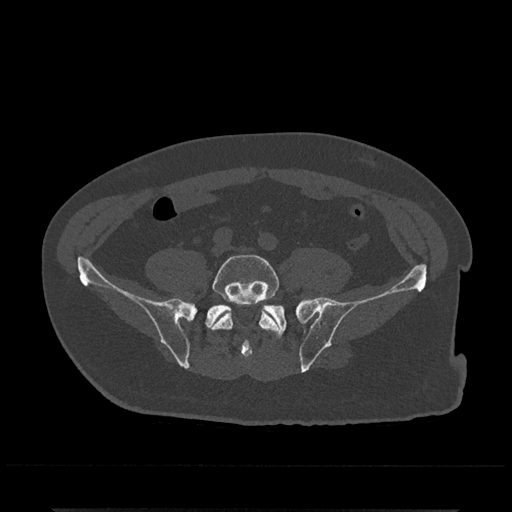
CT including the spine, one axial slice; 120 kVp; bone window (W 1800 / L 400 HU); 0.5 mm slice thickness; 512 × 512 image matrix, field of view 393 × 393 mm. Male patient, age 67 years. From the clinical record (not read from this slice): primary cancer: prostate.
Outlined on this slice (semi-automatically segmented with operator editing):
- L5 vertebra: bounding box <210,254,280,335> (left, top, right, bottom; pixels)